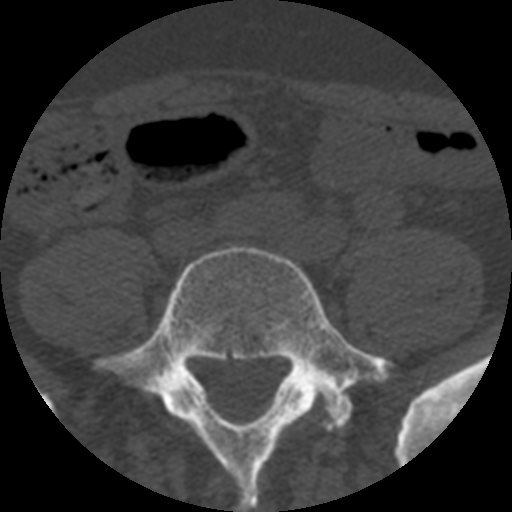
CT including the spine, one axial slice. Slice 65 of 508 in the series (ordered by position). Reconstruction kernel STANDARD. Bone window (W 1800 / L 400 HU). 512 × 512 image matrix. Patient age 57 years. Case-level facts recorded for this patient, not image findings: primary cancer: prostate.
Structures marked on this image (semi-automatically segmented with operator editing):
- L5 vertebra: bounding box (x1, y1, x2, y2) in pixels: (94, 245, 394, 512)